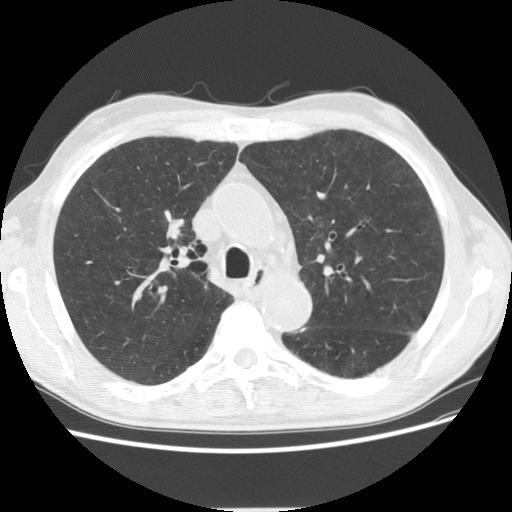
Low-dose screening chest CT, axial slice. First (baseline) screen. Lung window (W 1500 / L -600 HU). 2.5 mm slice thickness. Standard (soft-tissue) reconstruction kernel (STANDARD). Slice 45 of 135 in the series. Male, age 73 years at enrolment. Current smoker at enrolment.
Lesion marked by an expert reader, bounding box [x1, y1, x2, y2] px = [140, 194, 207, 261]. Screening reader's record for this exam (one nodule recorded; not confirmed to be the boxed lesion): non-calcified nodule or mass ≥4 mm, right upper lobe, 16 × 9 mm, spiculated (stellate) margins, soft tissue attenuation. Lung cancer was diagnosed 734 days after this screen: squamous cell carcinoma, NOS, right upper lobe, poorly differentiated (G3), stage IIIB (AJCC 6th edition), 56 mm at pathology.